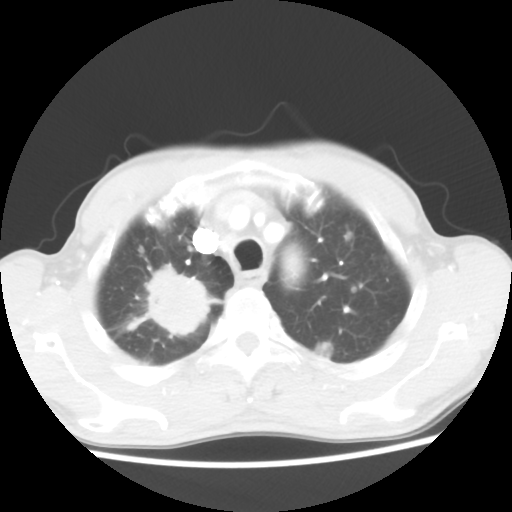
Chest CT, one axial slice. Position 43 of 52 along the scan axis. Lung window (W 1500 / L -600 HU). 5 mm slice thickness. 512 × 512 image matrix, field of view 323 × 323 mm. Male patient, age 66 years. From the clinical record (not read from this slice): clinical TNM (as recorded): T2 N0 M1a.
Annotated regions visible in this slice (rectangle marked by the reading radiologist):
- lung tumour (recorded histology: adenocarcinoma): bounding box (x1, y1, x2, y2) in pixels: (120, 259, 226, 344)